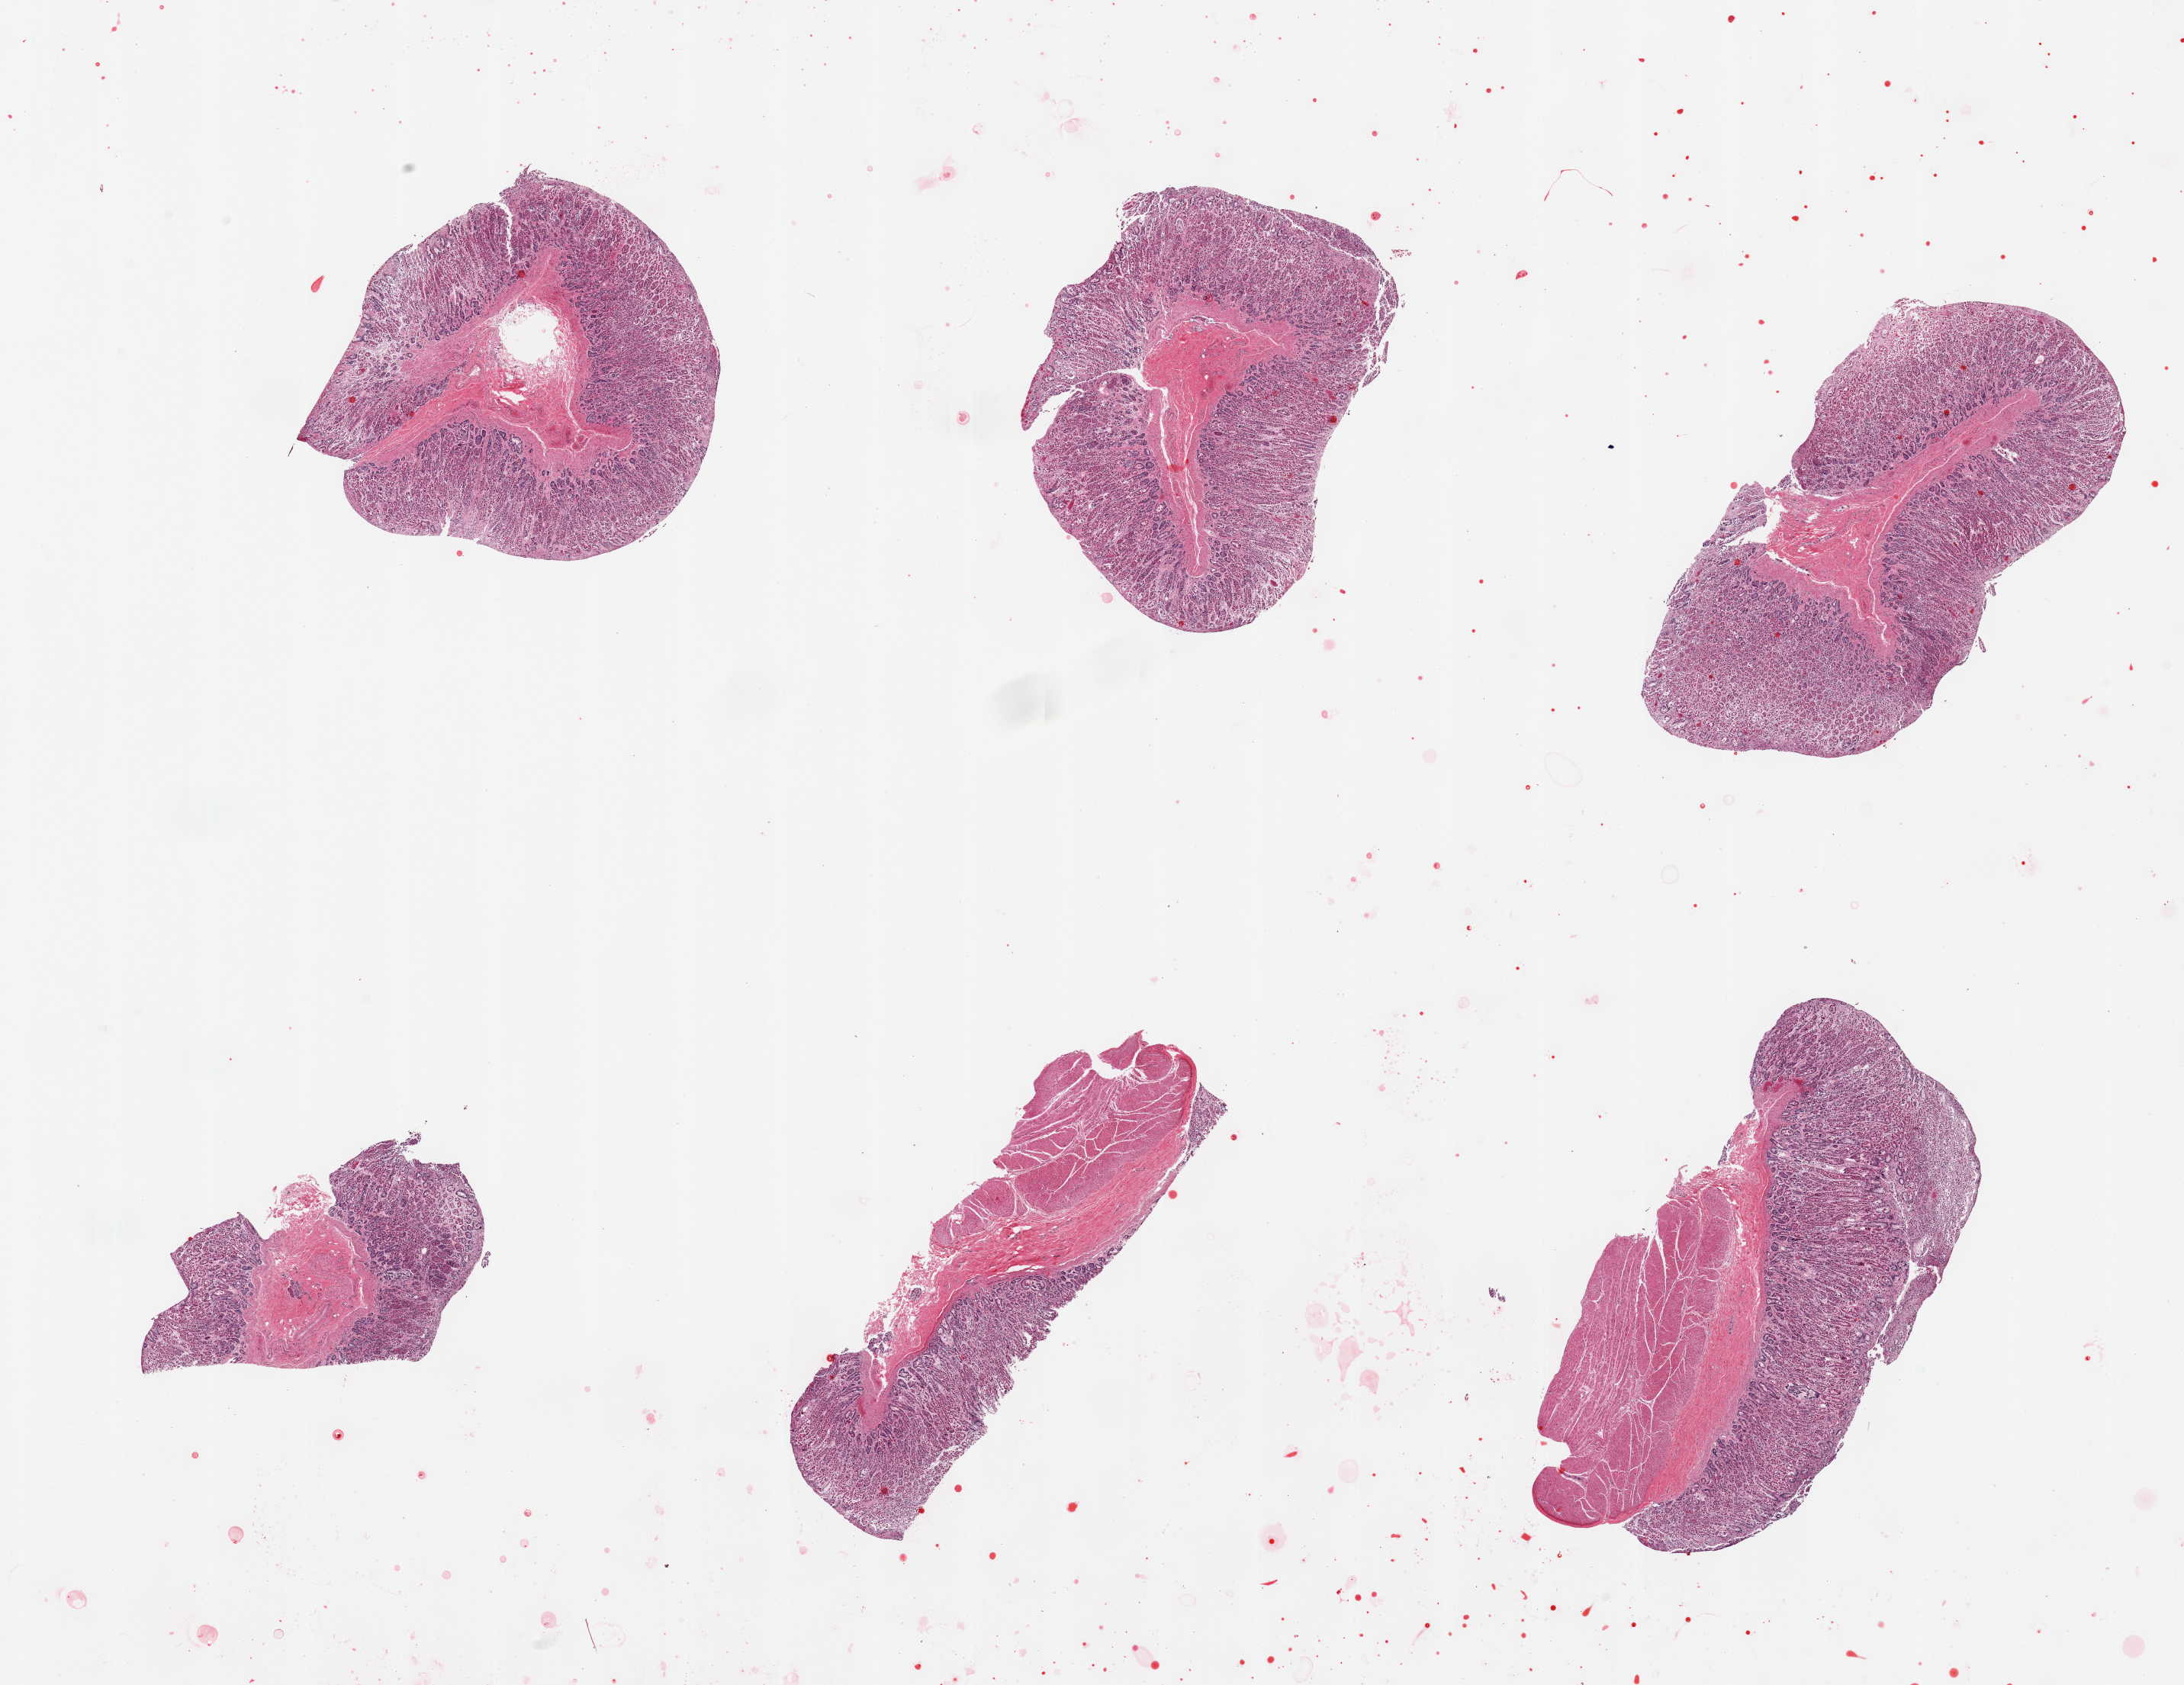
Hematoxylin and eosin (H&E) whole-slide image, brightfield — low-resolution overview of the scanned area, about 22.6 x 17.5 mm. PAXgene-fixed, paraffin-embedded tissue. Section of stomach (target tissue). Donor tissue sample. Donor: female.
- pathologist's review note for this sample: 6 pieces, mucosa up to ~1mm, 50-80% thickness but moderately advanced autolysis, particularly superficially